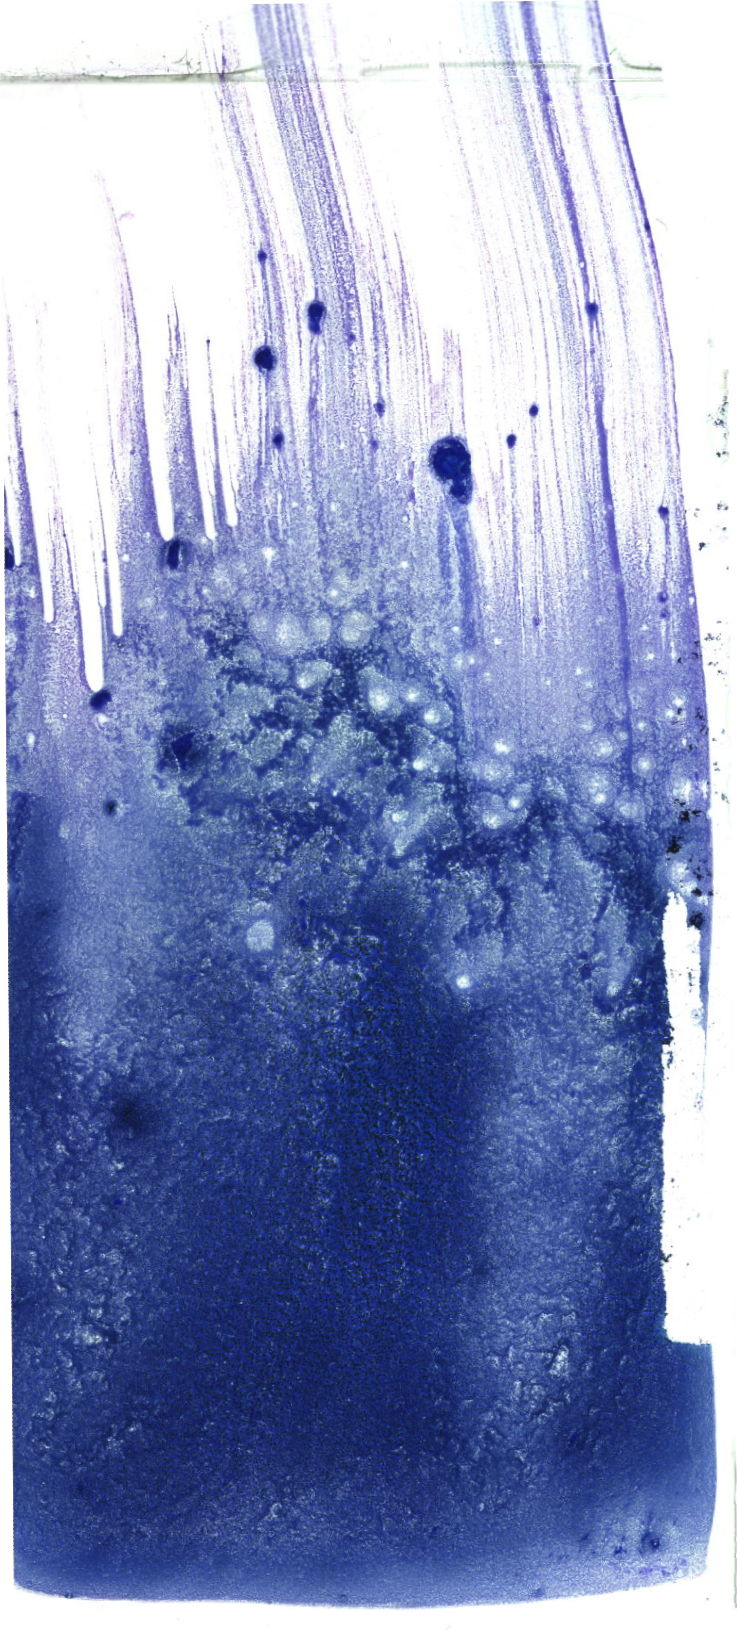
Whole-slide image of a May-Grünwald–Giemsa-stained bone marrow aspirate smear, whole scanned area (about 20.9 x 46.5 mm) shown as a low-resolution overview. Male patient.
Diagnosis: B Acute Lymphoblastic Leukemia.